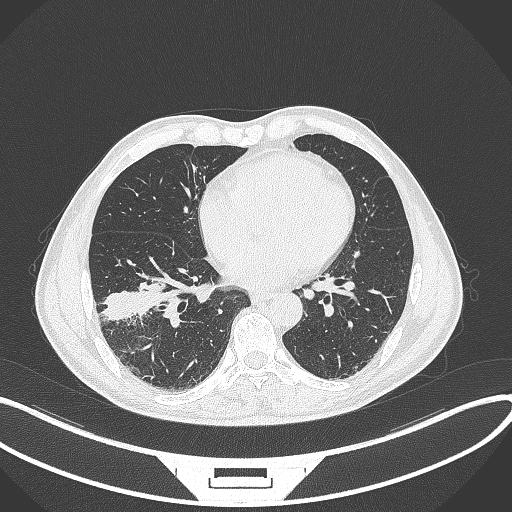
Chest CT, one axial slice; position 143 of 364 along the scan axis; lung window (W 1500 / L -600 HU); 1 mm slice thickness; 512 × 512 image matrix, field of view 400 × 400 mm. Patient: male, 58 years. Case-level facts recorded for this patient, not image findings: clinical TNM (as recorded): T3 N0 M0; histopathological grade: G2.
Structures marked on this image (rectangle marked by the reading radiologist):
- lung tumour (recorded histology: squamous cell carcinoma): bounding box [x1, y1, x2, y2] px = [98, 282, 165, 321]